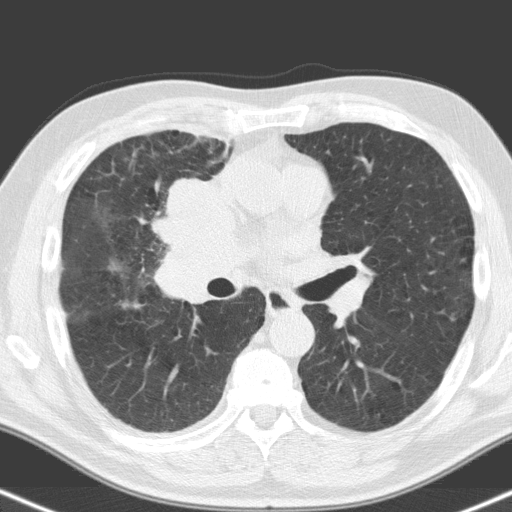
Low-dose screening chest CT, one axial slice. Slice 91 of 160 in the series (ordered by position). Lung window (W 1500 / L -600 HU). 3.2 mm slice thickness. 512 × 512 image matrix, field of view 324 × 324 mm.
Structures marked on this image (outlined manually by an expert reader):
- lesion 1 (tumor, hilum of right lung): bounding box (x1, y1, x2, y2) in pixels: (158, 179, 236, 303)